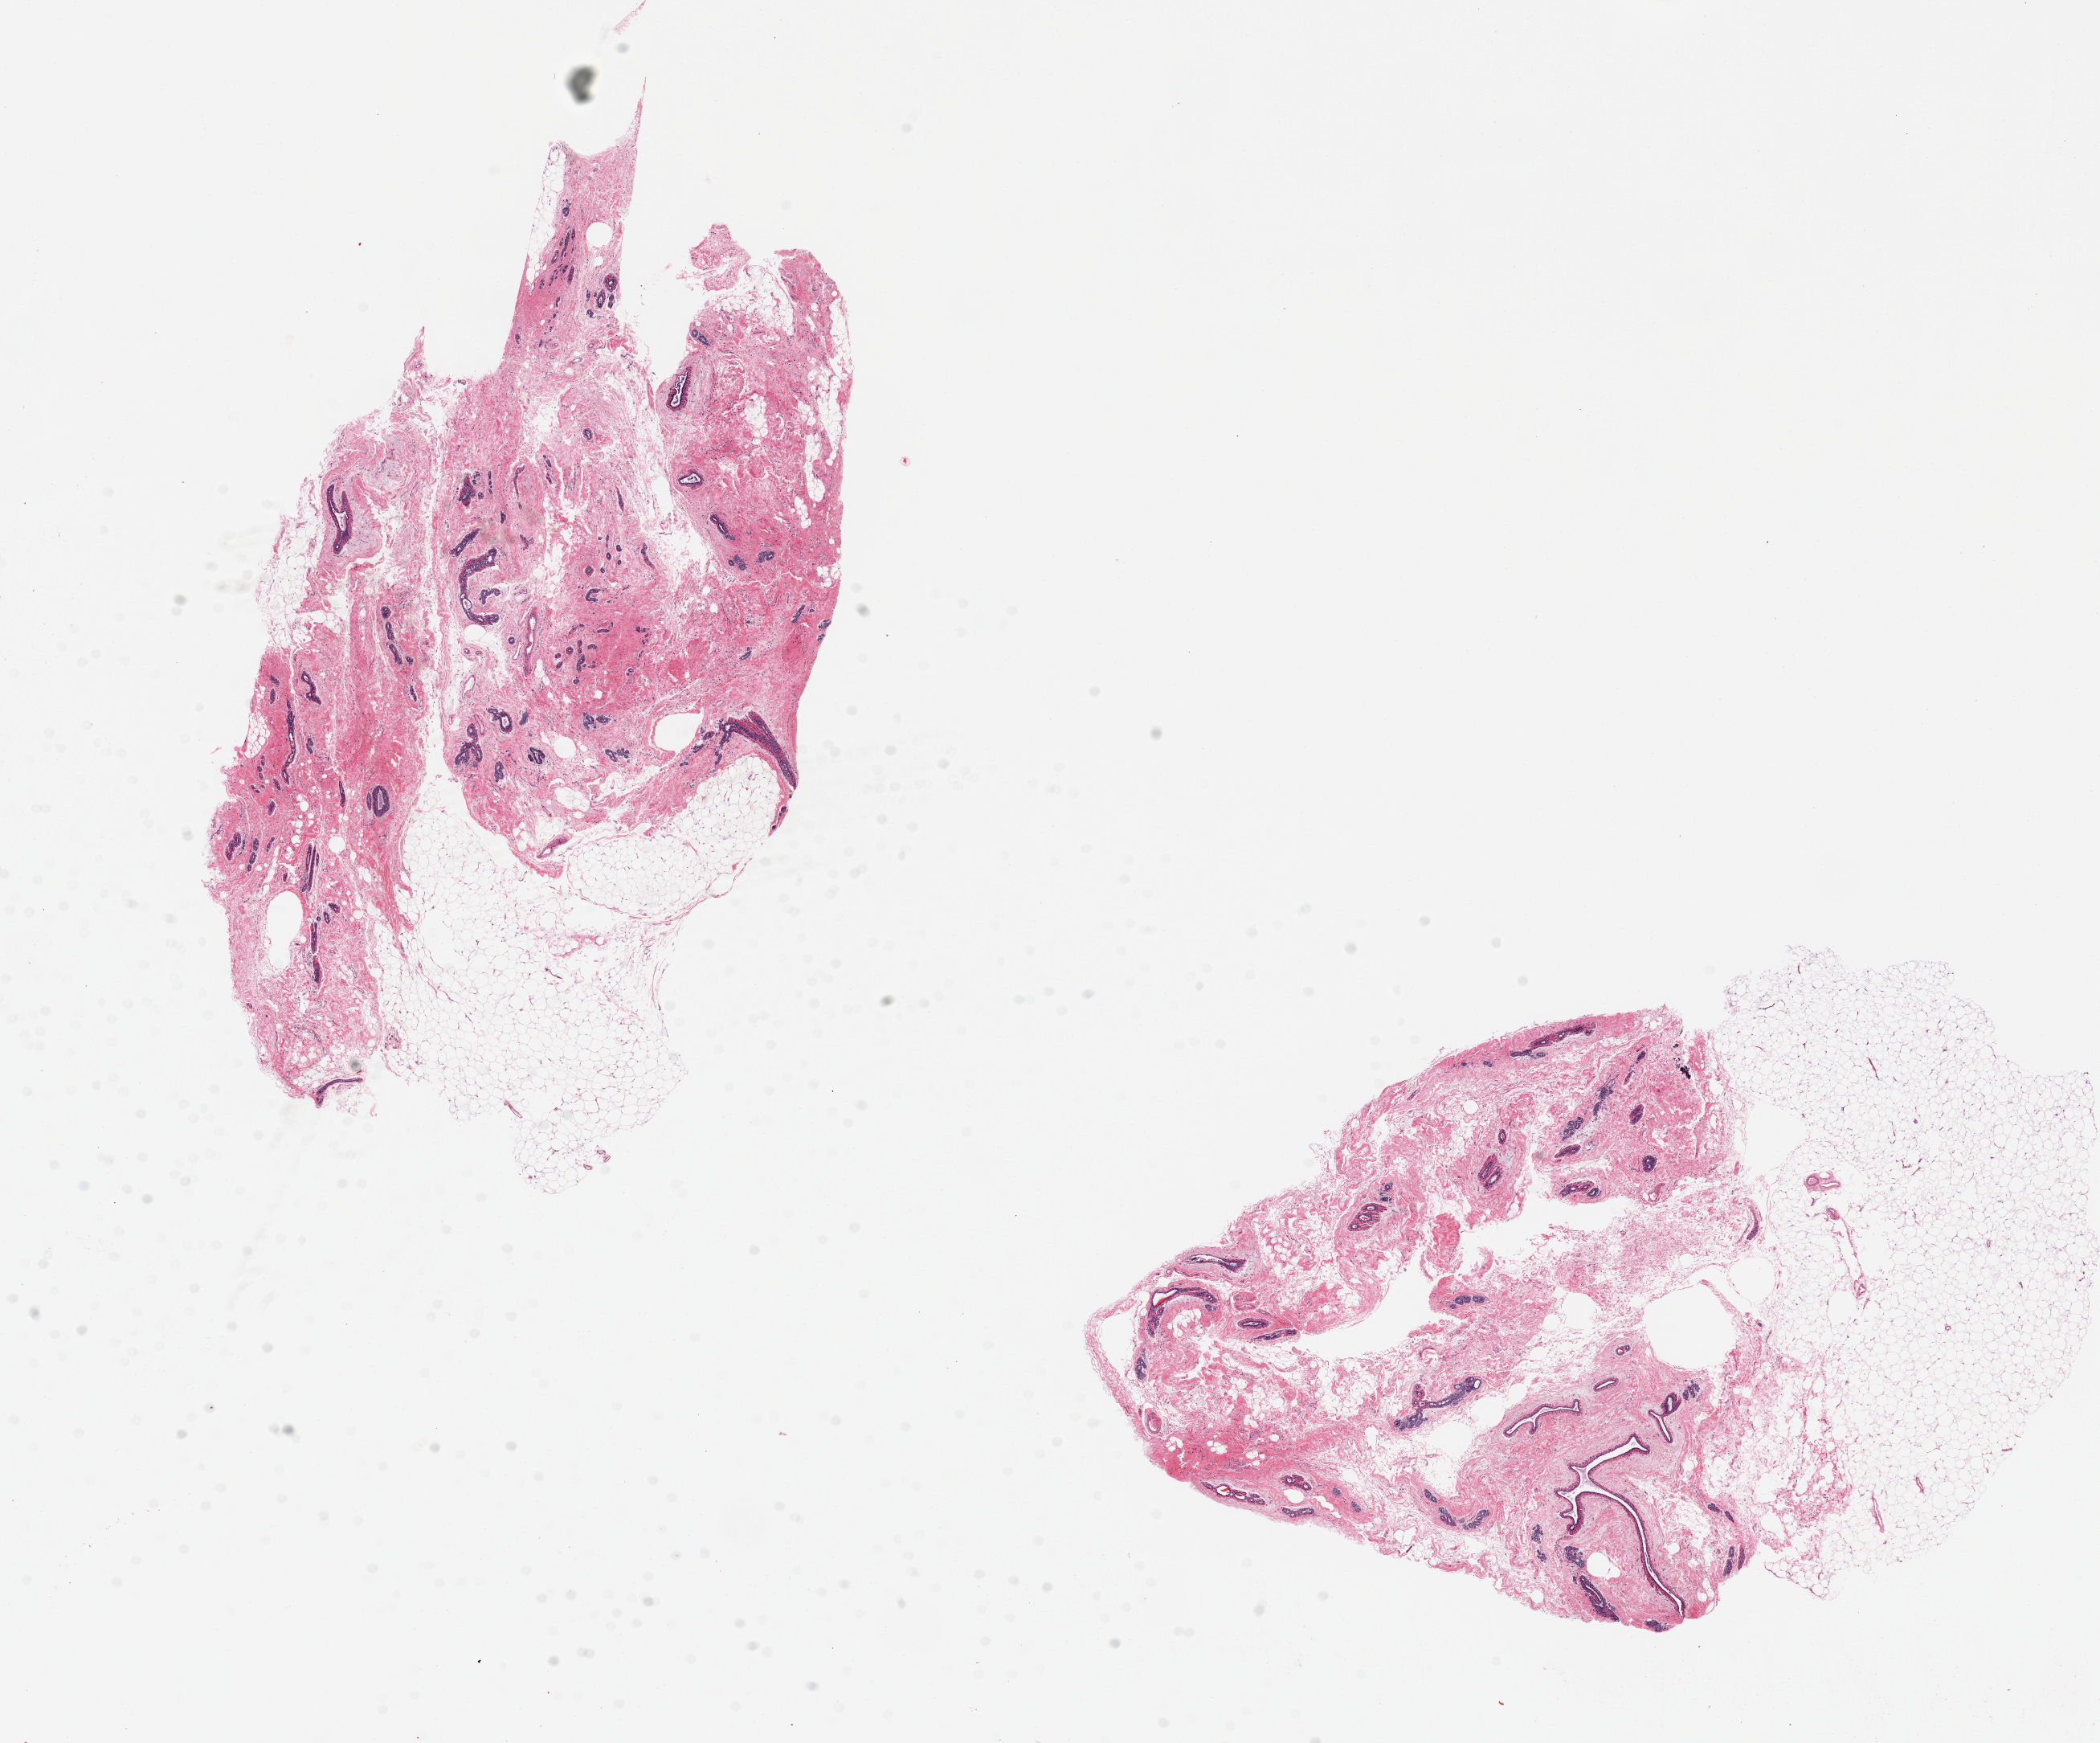
Whole-slide image, H&E stain, a low-resolution overview of the entire scanned area, about 20.7 x 17.2 mm, PAXgene-fixed, paraffin-embedded tissue, sampled site (target tissue): breast, donor tissue sample. Donor sex: female.
Pathologist's review note for this sample: 2 pieces, 11x7 & 10x6.5mm; atrophic TDLUs abundant.